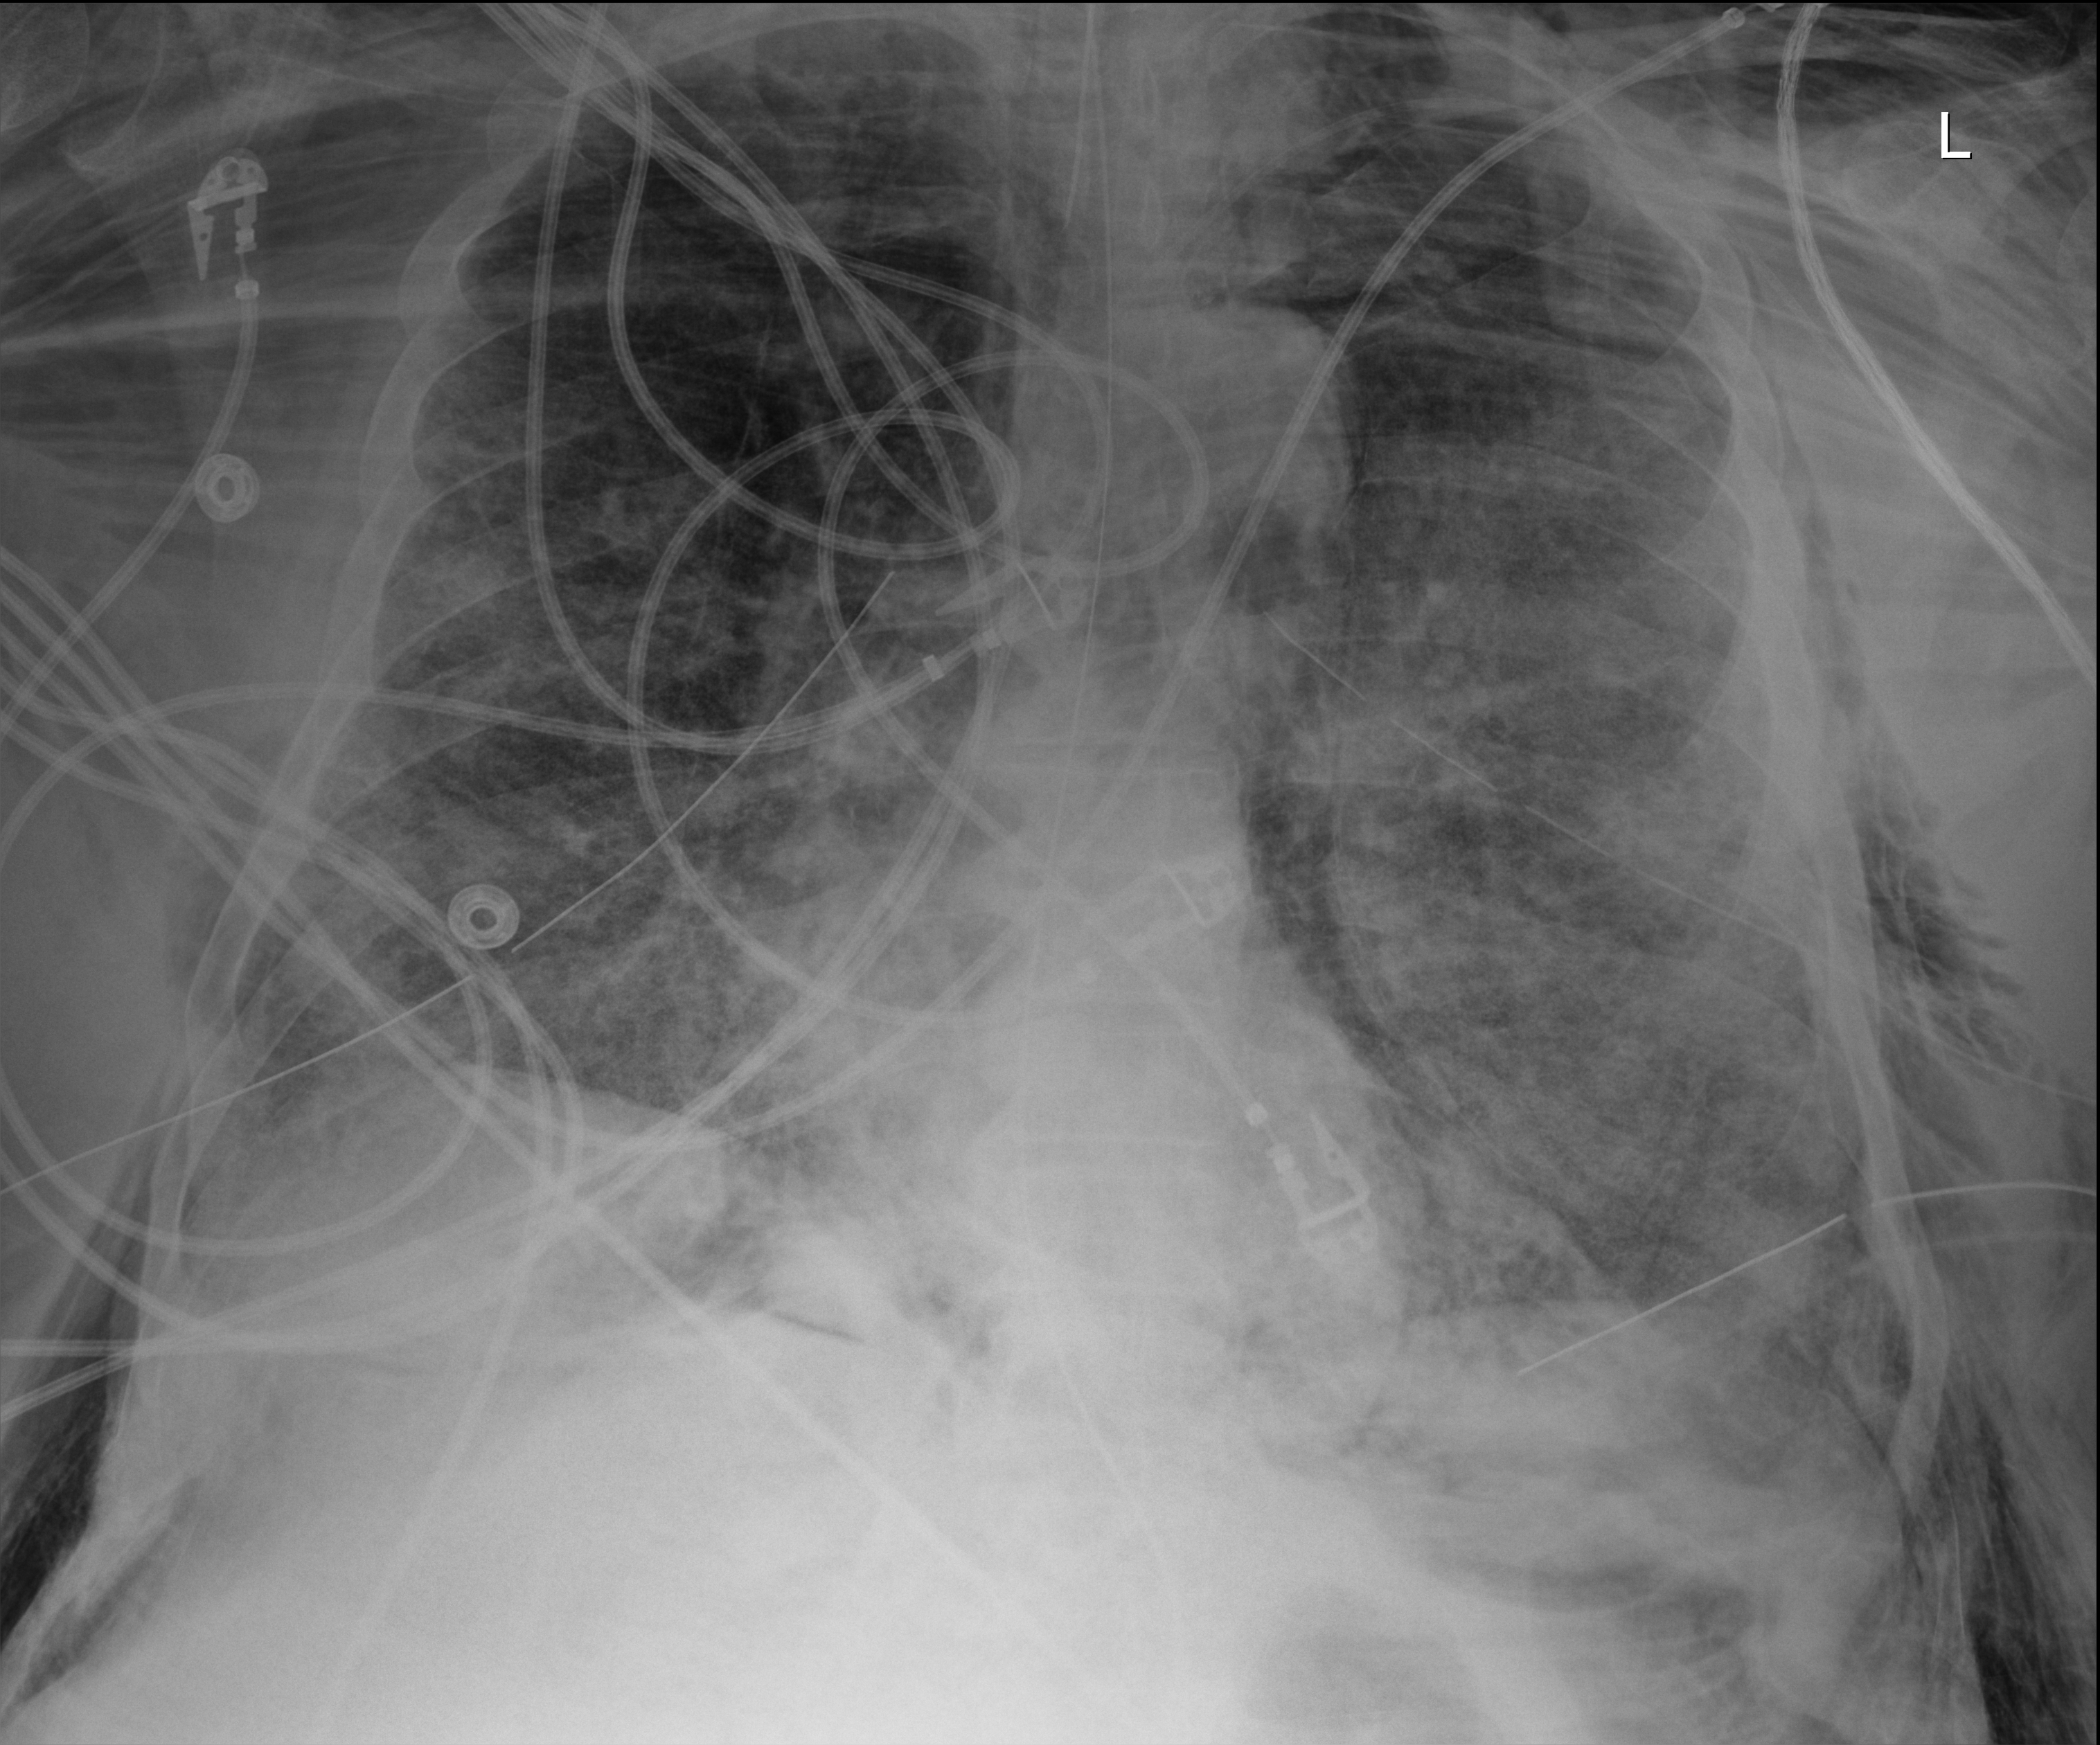
Portable chest radiograph. Patient hospitalised with COVID-19, aged 18–59 years.
Hospital-stay facts (about this admission, not read from this image; timing relative to this image not recorded): length of hospital stay: 28 days.